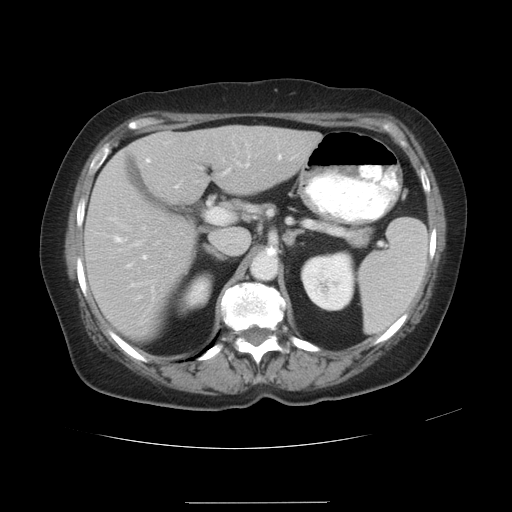
Contrast-enhanced abdominal CT, one axial slice. Position 18 of 32 along the scan axis. Reconstruction kernel STANDARD. Soft-tissue window (W 400 / L 40 HU). 7.5 mm slice thickness. 512 × 512 image matrix. Female patient, age 65 years. Case-level facts recorded for this patient, not image findings: diagnosis: colorectal cancer liver metastases, imaged before liver resection; multiple liver metastases: yes; largest metastasis: 1.7 cm; disease in both lobes: no.
Structures marked on this image (outlined manually by an expert reader):
- liver: bounding box (x1, y1, x2, y2) in pixels: (87, 126, 317, 337)
- planned liver remnant (the part of the liver to remain after resection): (86, 131, 222, 337)
- portal vein (with intrahepatic branches): (113, 158, 250, 260)